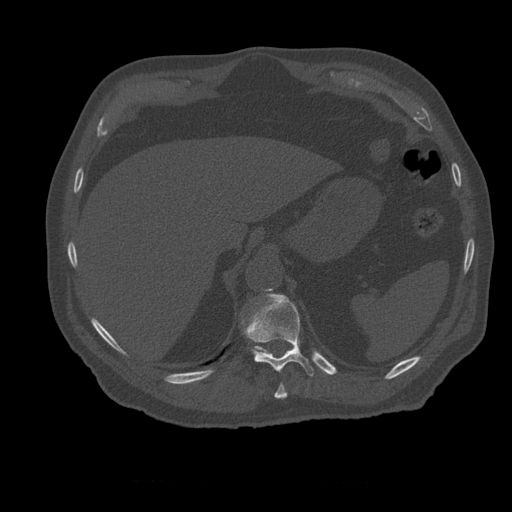
CT including the spine, one axial slice. Position 281 of 399 along the scan axis. Bone window (W 1800 / L 400 HU). 1.25 mm slice thickness. 512 × 512 image matrix, field of view 407 × 407 mm. Patient age 73 years. Case-level facts recorded for this patient, not image findings: primary cancer: prostate.
Structures marked on this image (semi-automatically segmented with operator editing):
- T10 vertebra: bounding box <274,384,287,399> (left, top, right, bottom; pixels)
- T11 vertebra: <244,294,314,376>
- T12 vertebra: <244,303,262,353>